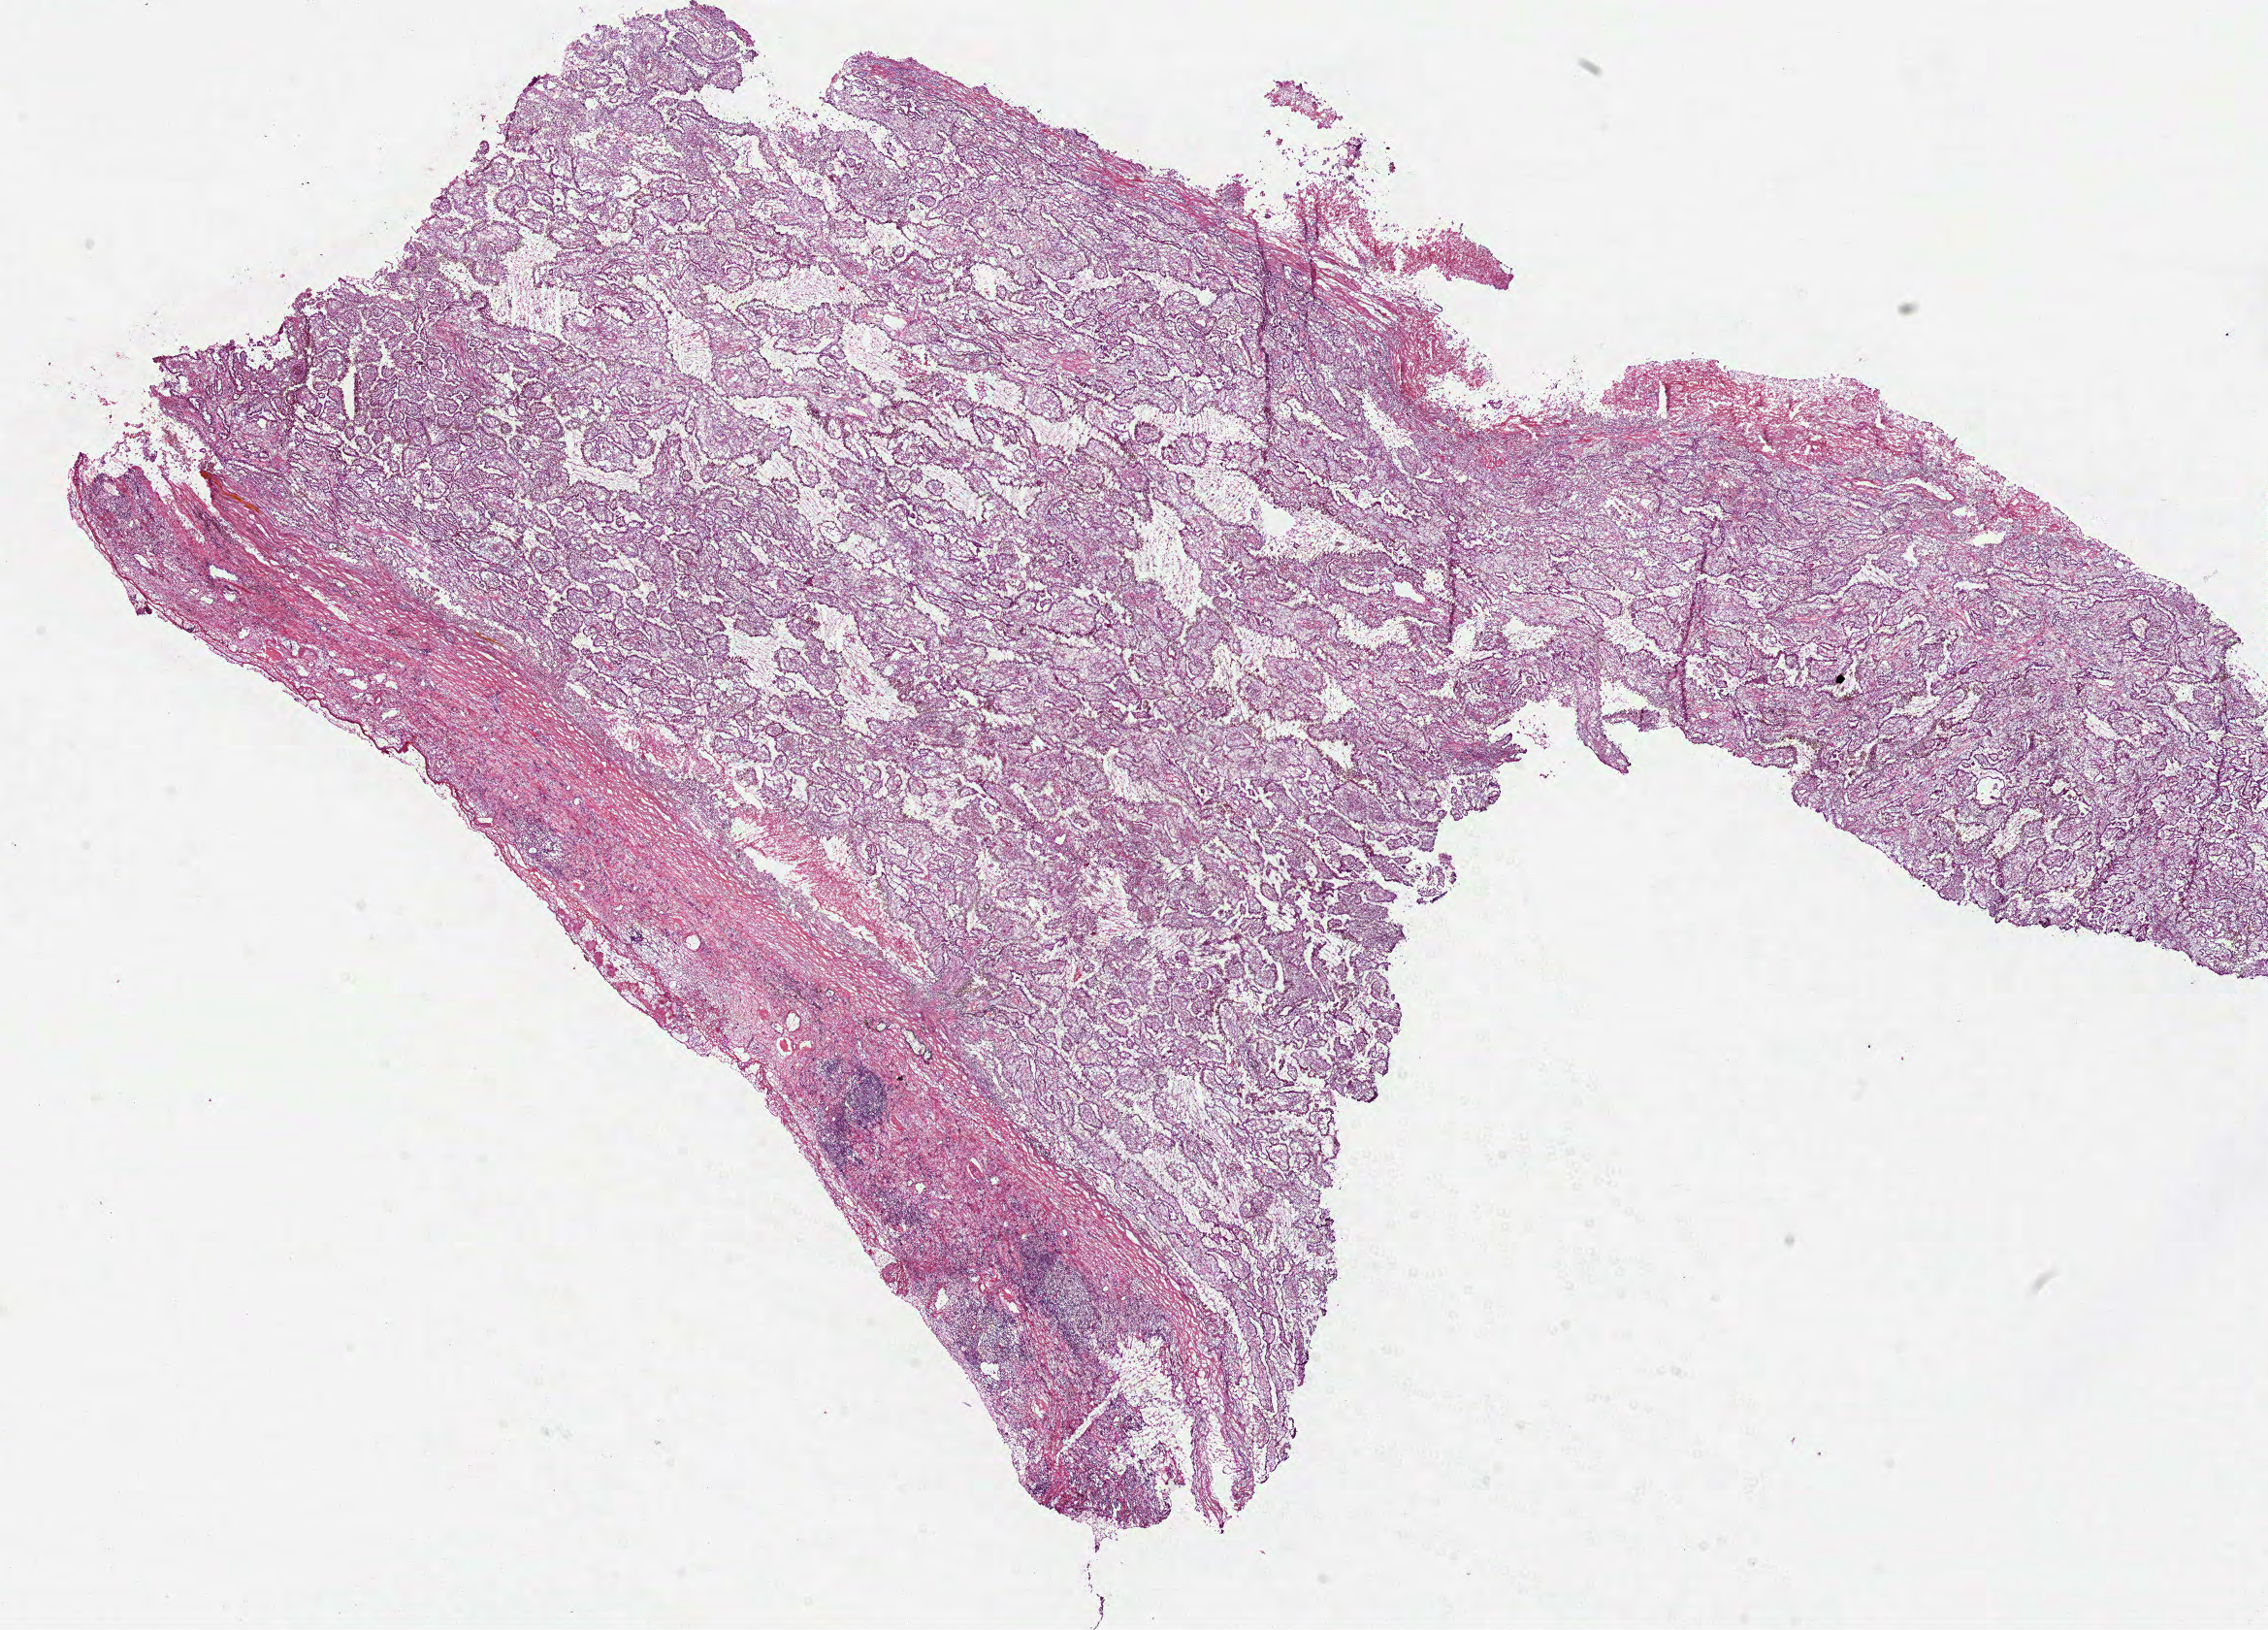
Whole-slide histology image, H&E — a low-resolution overview of the entire scanned area, about 18.9 x 13.5 mm (slide scanned at 40x), frozen section from the bottom of the tissue portion, primary tumour sample from the kidney. Patient: male, age at initial diagnosis 66 years. Pathologist review of this section (percent, as recorded): tumour cells 90%, tumour nuclei 70%, normal cells 0%, stromal cells 10%, necrosis 0%. Infiltration values recorded for this section: lymphocyte infiltration 1%, monocyte infiltration 20%, neutrophil infiltration 0%.
AJCC pathologic stage: I. Pathologic diagnosis: Papillary adenocarcinoma, NOS.